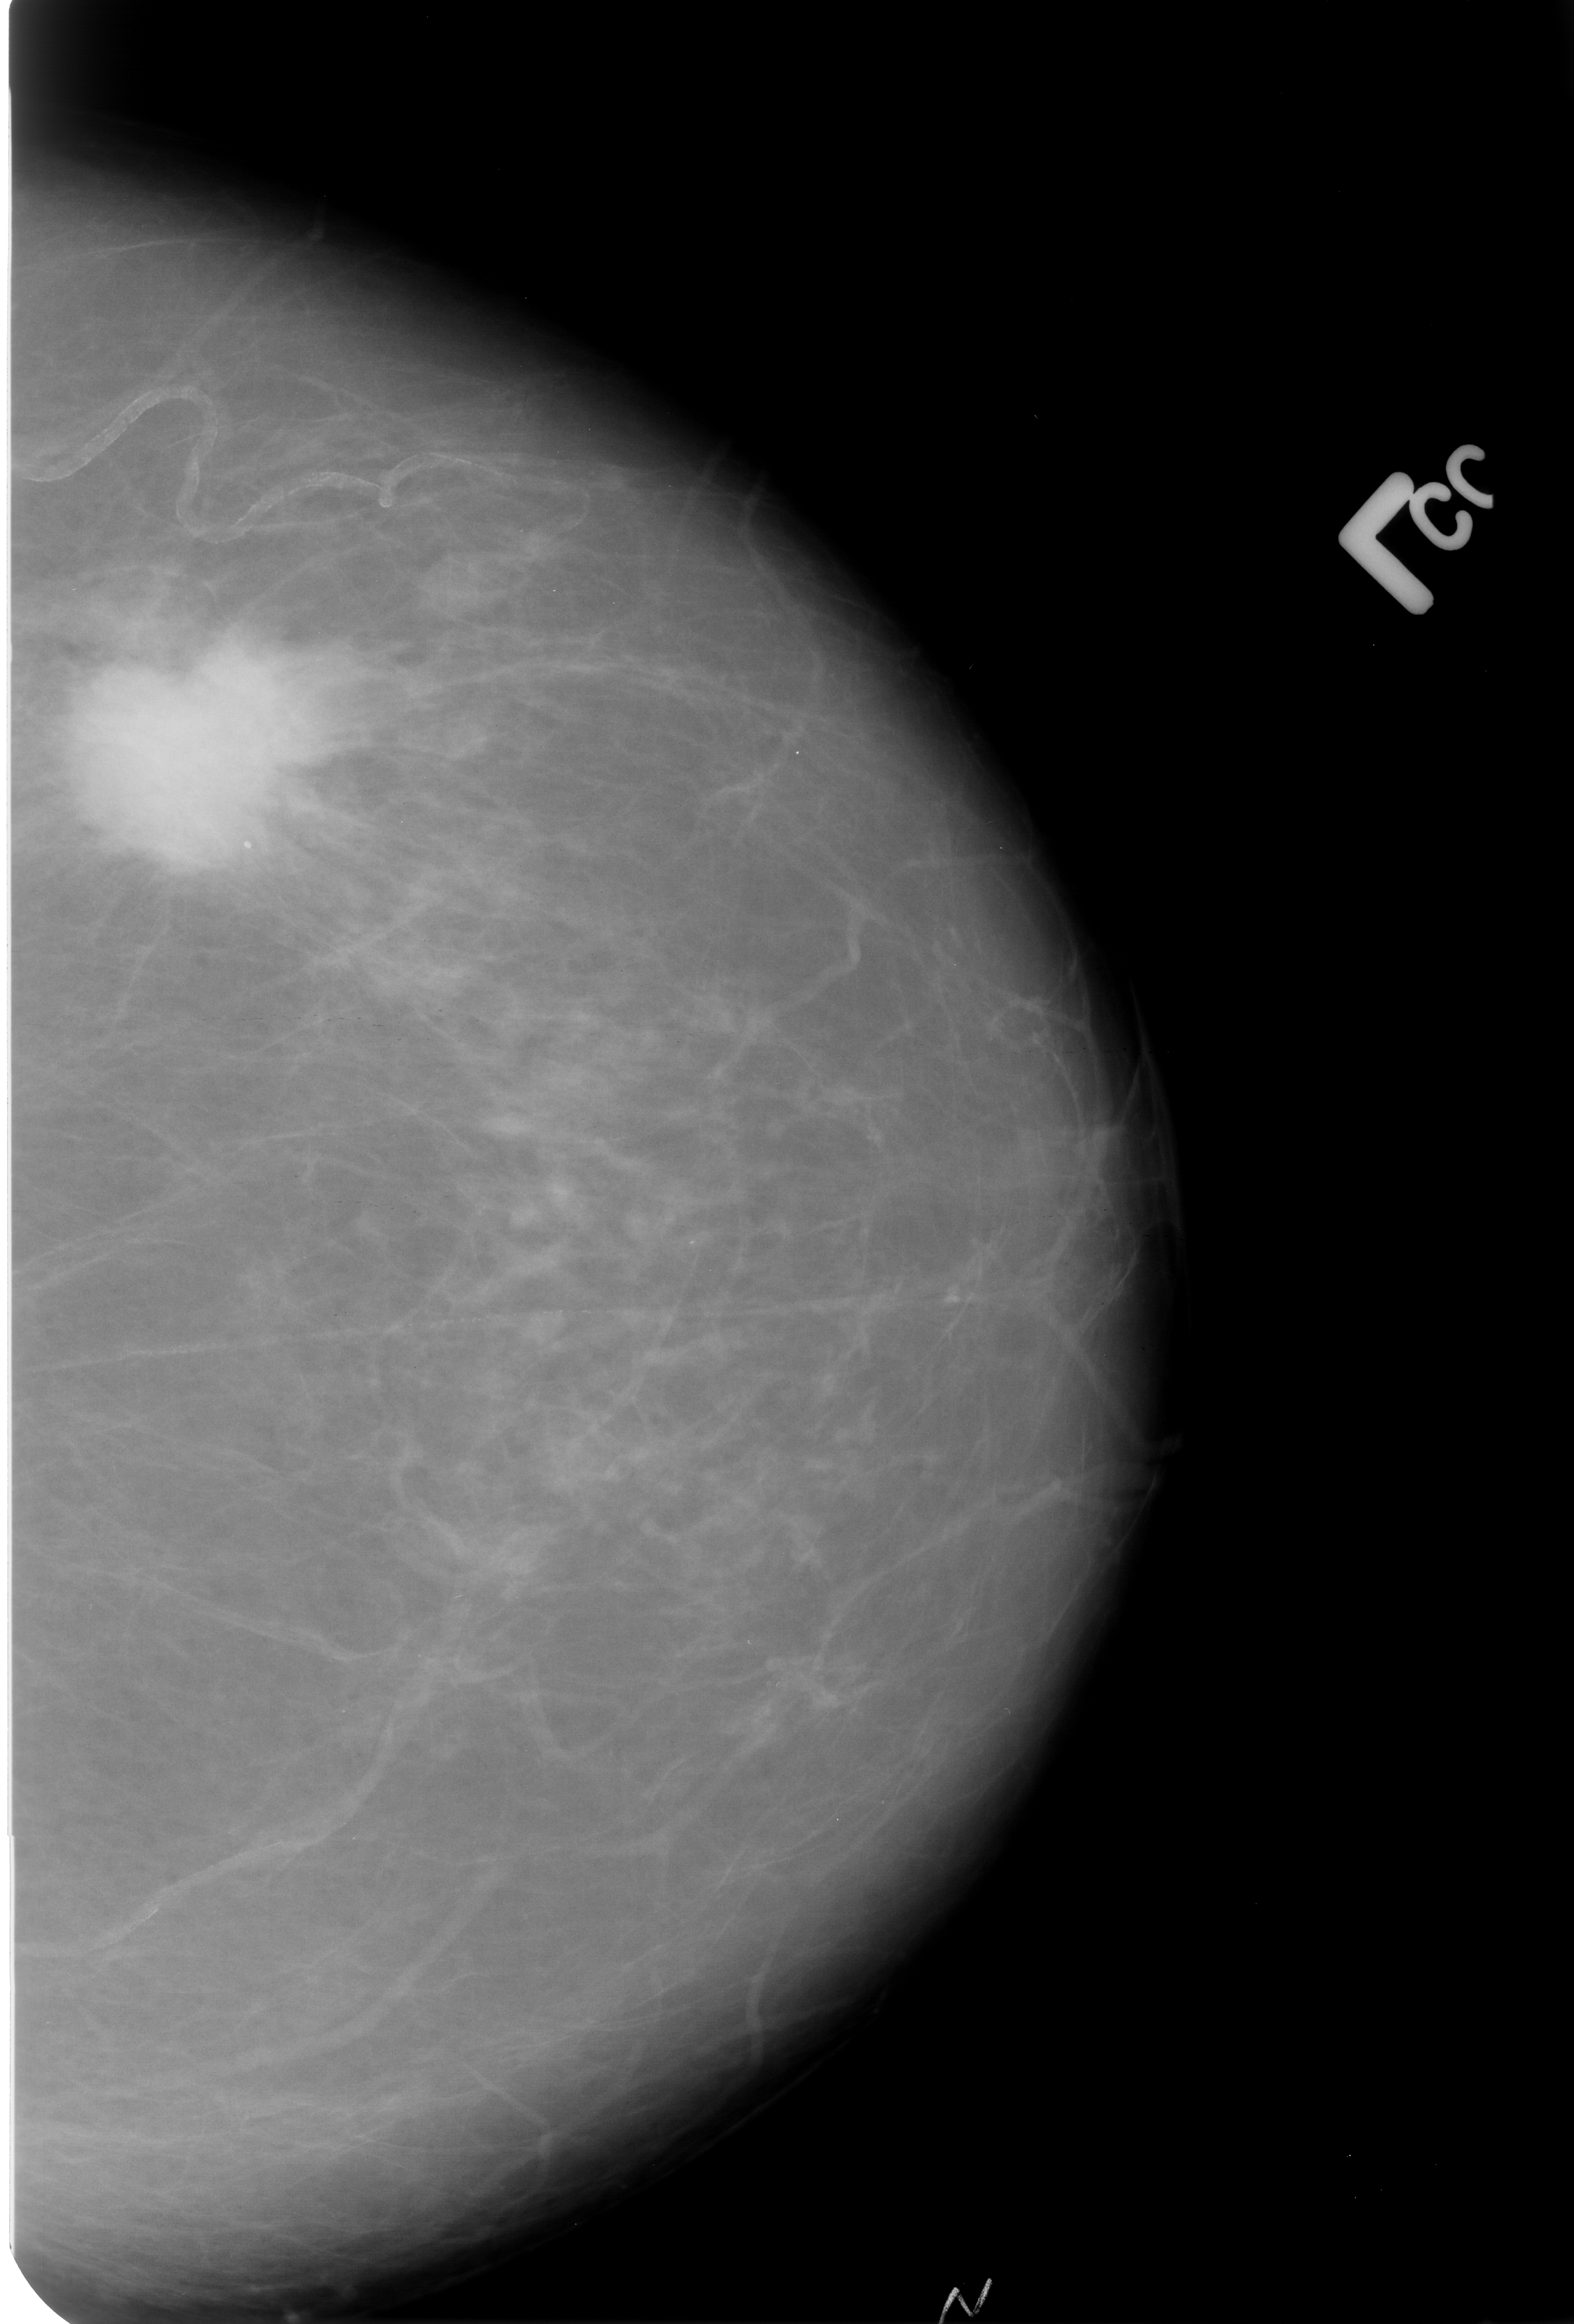
Scanned film-screen mammogram. Left breast. CC view. BI-RADS breast density category 2 (scale 1–4). 1574 × 2324 image matrix.
Marked abnormalities (boxes around the expert regions of interest):
- mass, shape round / irregular / architectural distortion, margins spiculated; BI-RADS assessment category 5; subtlety rating 5 on a 1 (subtle) to 5 (obvious) scale; pathology result (as recorded, not read from the image): malignant: bounding box [x1, y1, x2, y2] px = [51, 611, 340, 896]